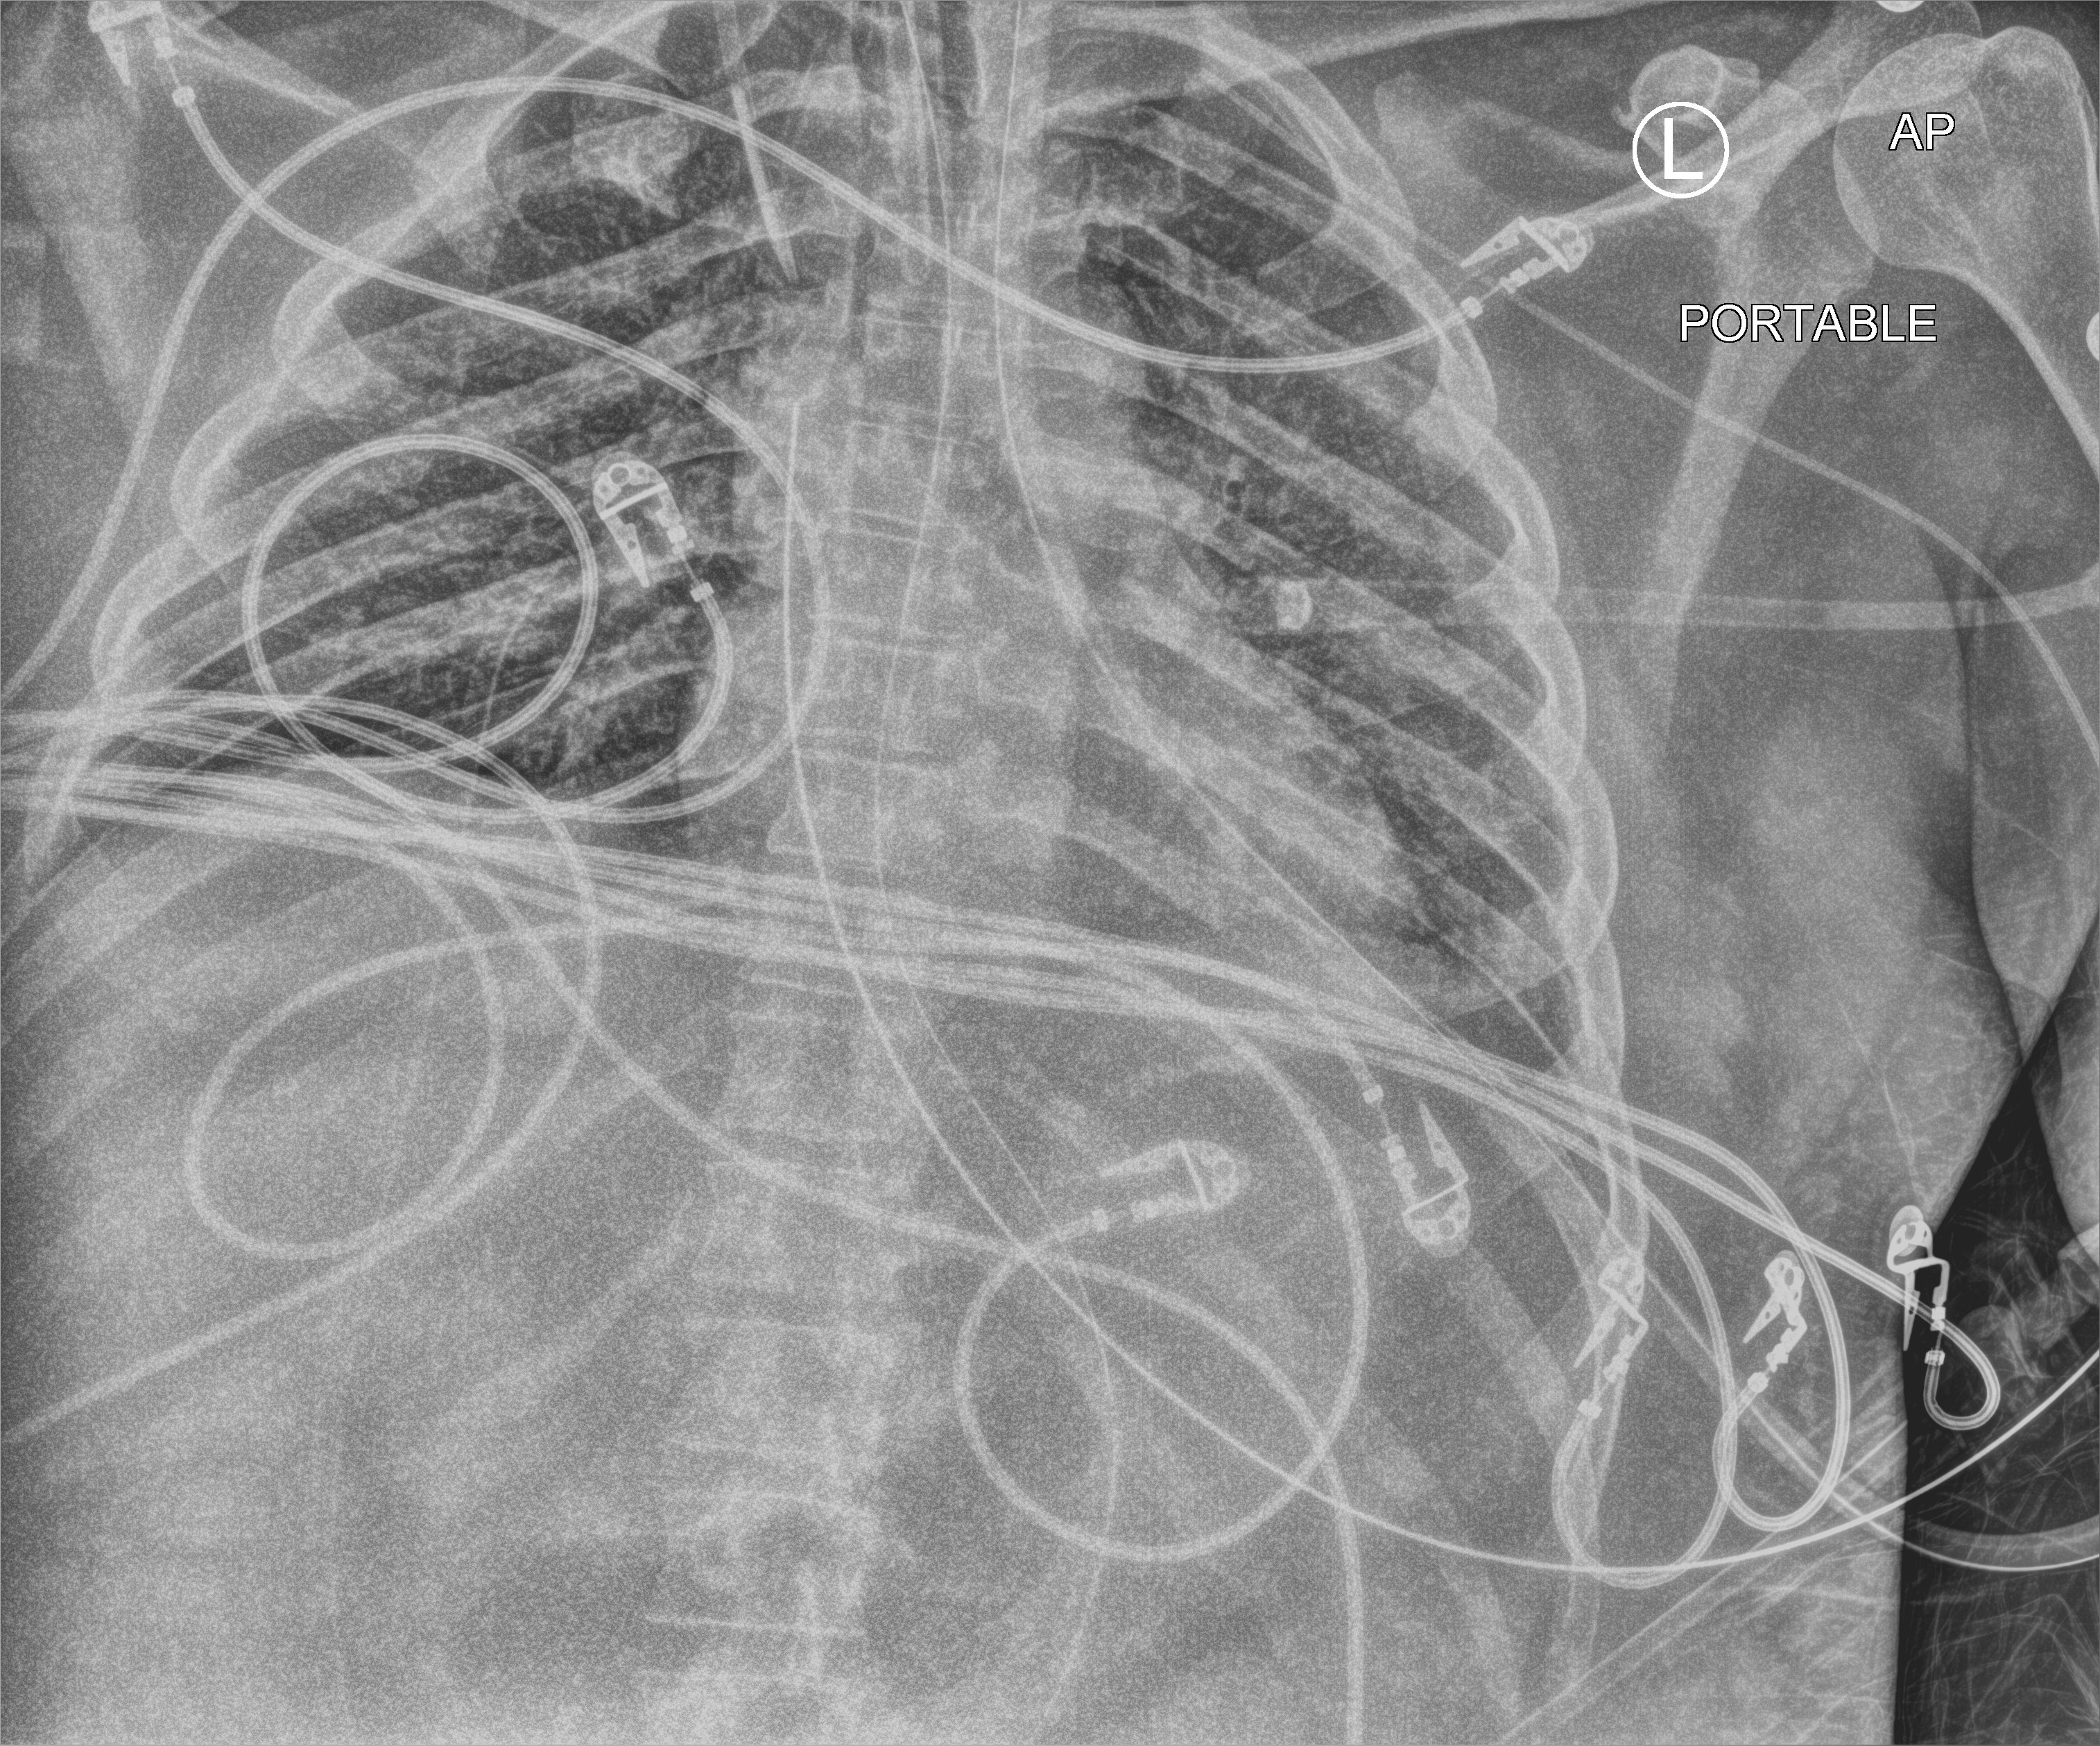
Portable chest radiograph. Adult patient hospitalised with COVID-19, age 18–59 years.
Admission-level facts for this patient (not findings on this image; timing relative to this image not recorded): admitted to intensive care during this hospital stay: yes.